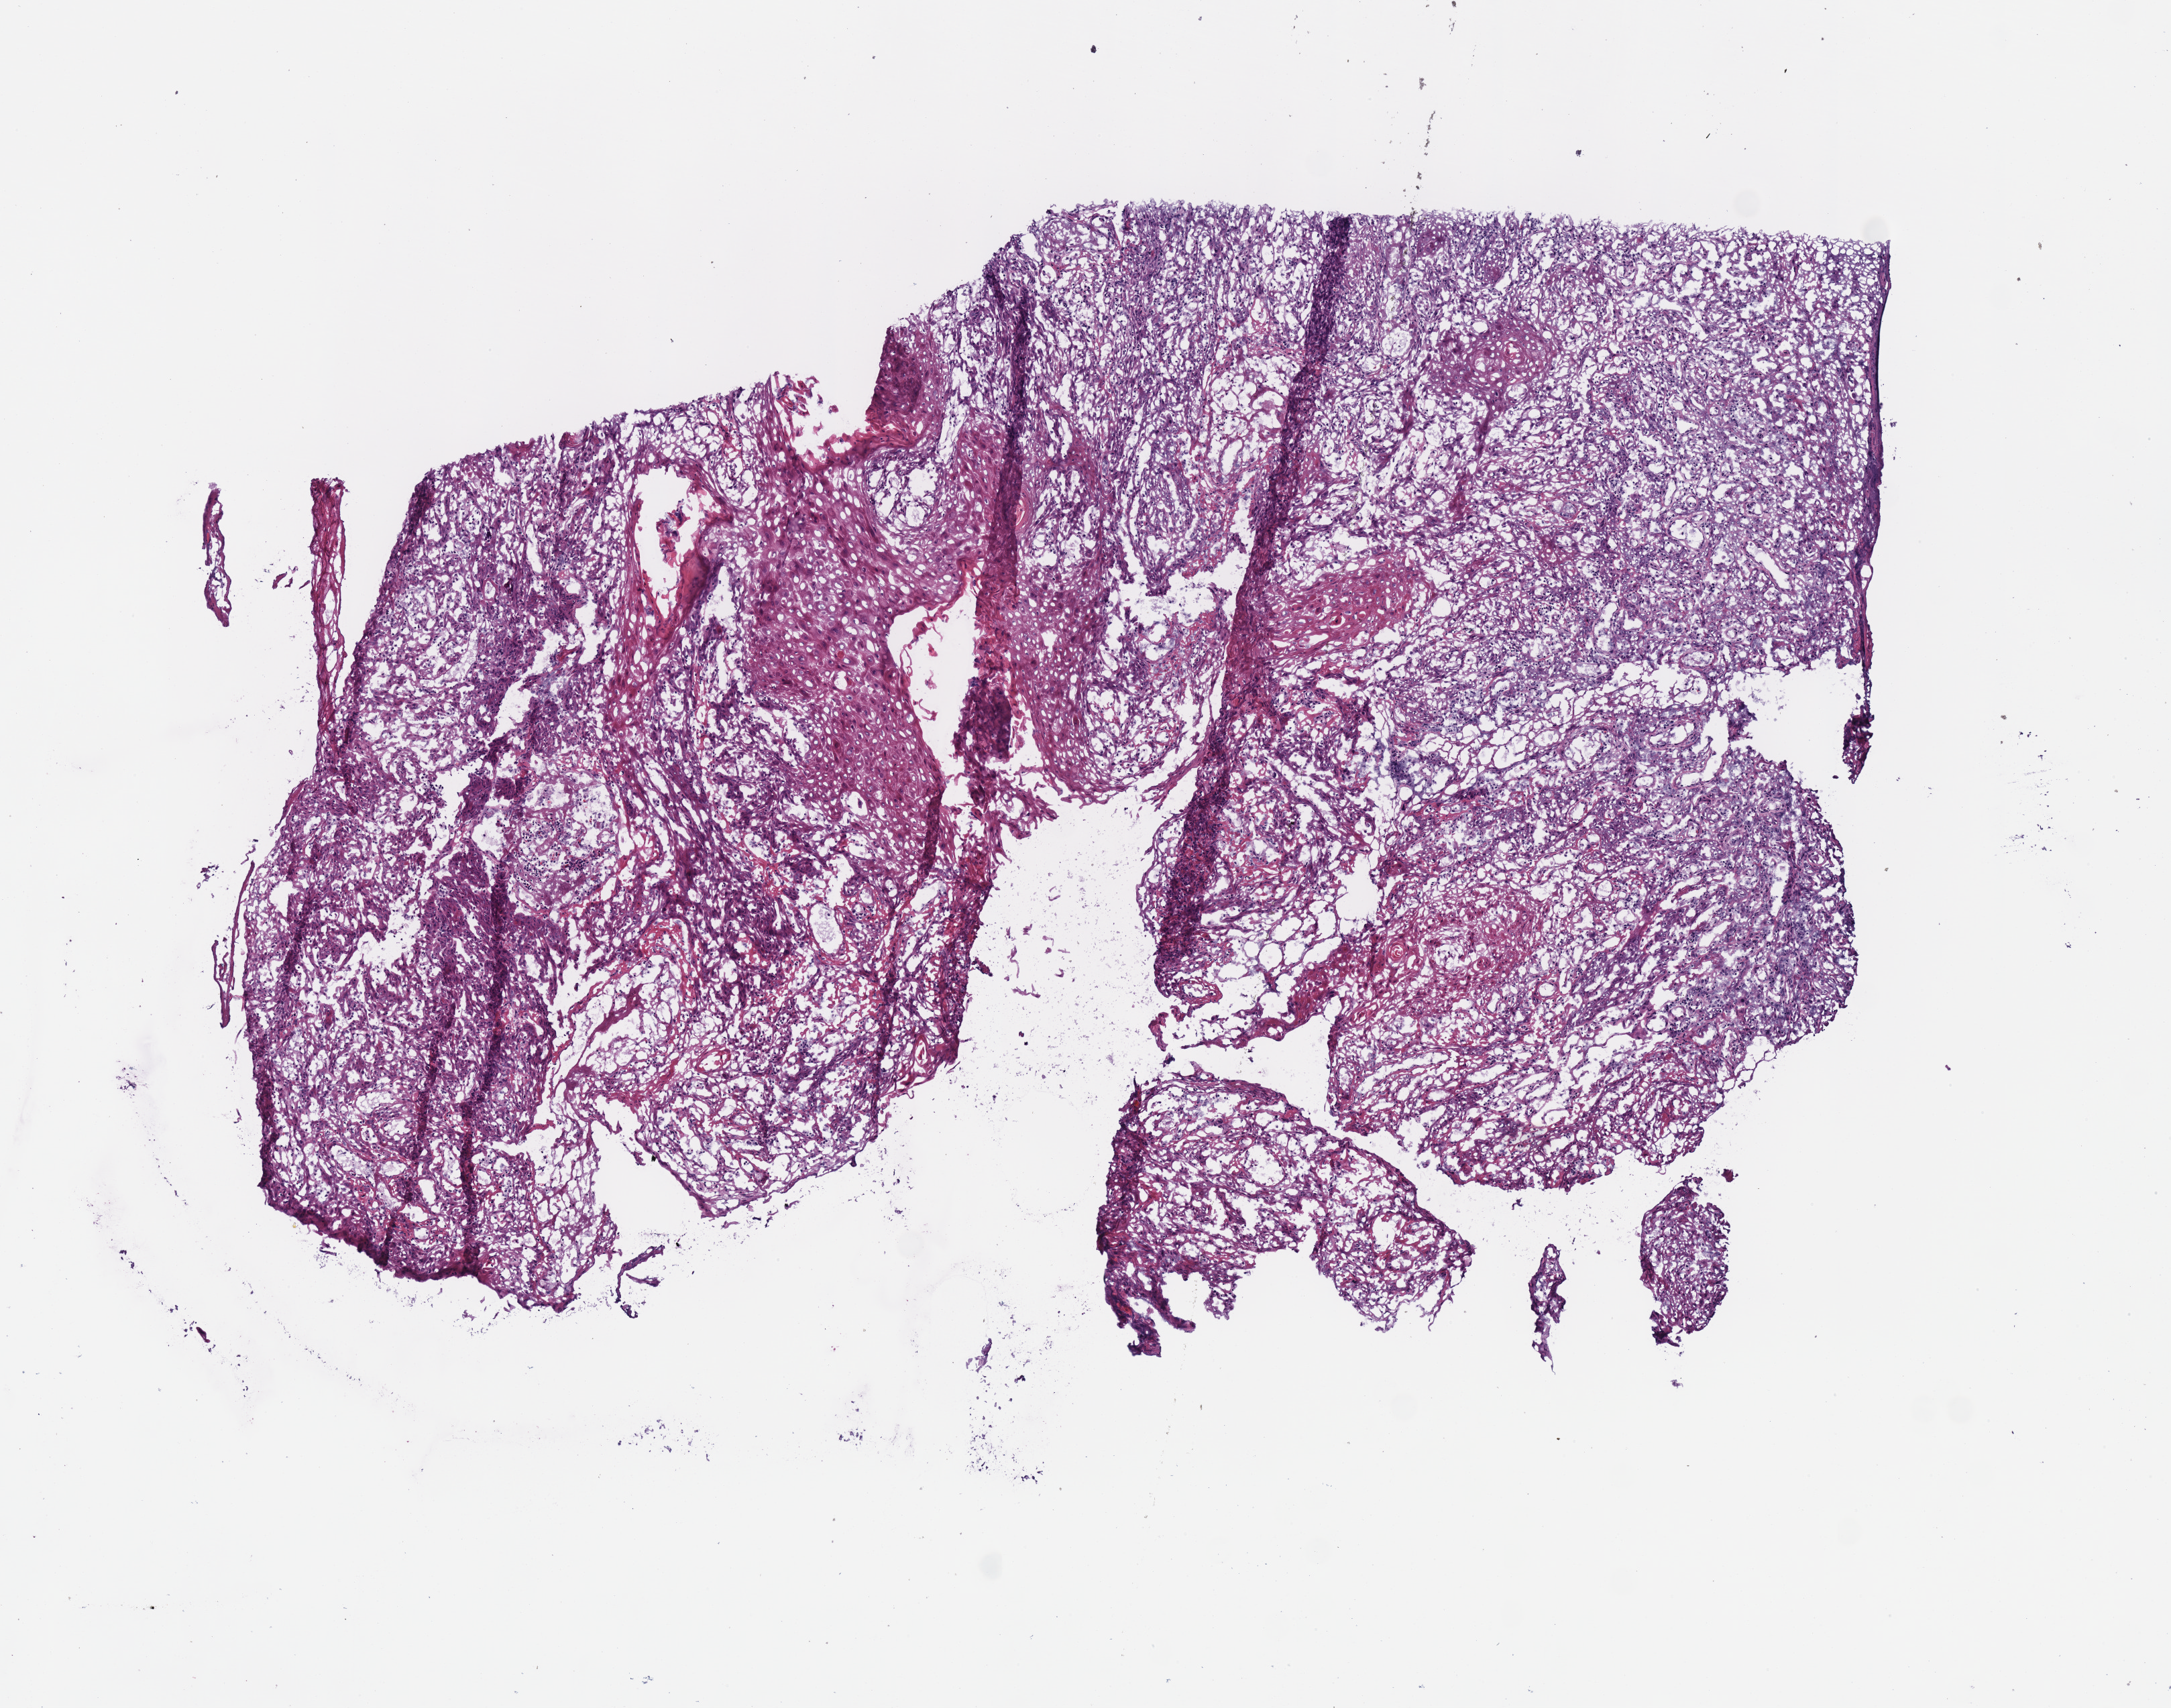
Digitized Hematoxylin and eosin (H&E) stained tissue section (whole slide) — low-resolution overview of the scanned area, about 6.4 x 5.0 mm (slide scanned at 40x), frozen section from the bottom of the tissue portion, primary tumour sample from the head and neck. Male, age 63 years at initial diagnosis. Histologic grade: G3 (poorly differentiated). Composition of this section per pathologist review: tumour cells 90%, tumour nuclei 65%, normal cells 0%, stromal cells 10%, necrosis 0%.
Pathologic diagnosis: Squamous cell carcinoma, NOS (mouth, NOS). AJCC pathologic stage: I (7th edition).